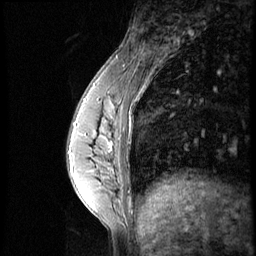
Breast MRI (dynamic contrast-enhanced), one sagittal slice; position 17 of 56 along the scan axis; dynamic contrast-enhanced series, image 2 of 4 at this slice position (ordered by acquisition); 1.5 T; TE 4.2 ms, TR 8.9 ms; 256 × 256 image matrix, field of view 200 × 200 mm. Patient: female, 35 years. From the clinical record (not read from this slice): setting: breast cancer imaged before/during neoadjuvant chemotherapy; receptor status: HER2-positive.
Outlined on this slice (semi-automatically segmented with operator editing):
- analysis volume of interest (the breast-tissue region the enhancement analysis was run in; not a lesion): bounding box [x1, y1, x2, y2] px = [73, 111, 131, 164]
- tumour enhancement mask (voxels above the 140 % enhancement threshold inside the analysis volume of interest): [75, 113, 114, 153]